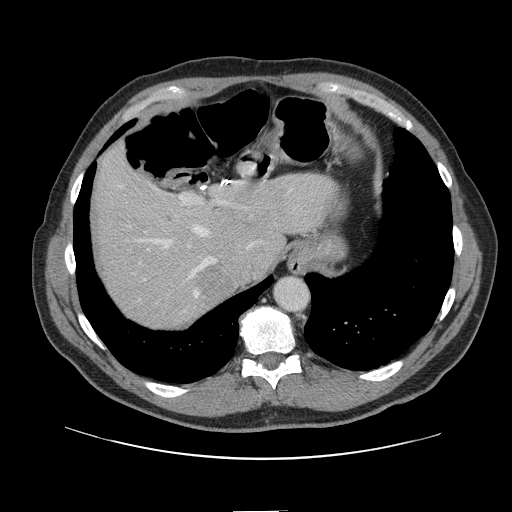
Contrast-enhanced abdominal CT, one axial slice; position 113 of 161 along the scan axis; 120 kVp; intravenous contrast given; soft-tissue window (W 400 / L 40 HU); 2.5 mm slice thickness; 512 × 512 image matrix. Male patient, age 66 years. From the clinical record (not read from this slice): diagnosis: colorectal cancer liver metastases, imaged before liver resection; multiple liver metastases: no; largest metastasis: 3.5 cm; disease in both lobes: no.
Annotated regions visible in this slice (outlined manually by an expert reader):
- hepatic veins: bounding box <120,185,224,298> (left, top, right, bottom; pixels)
- liver: <96,149,326,328>
- planned liver remnant (the part of the liver to remain after resection): <95,150,328,304>
- portal vein (with intrahepatic branches): <179,195,248,248>
- liver metastasis: <192,264,225,302>